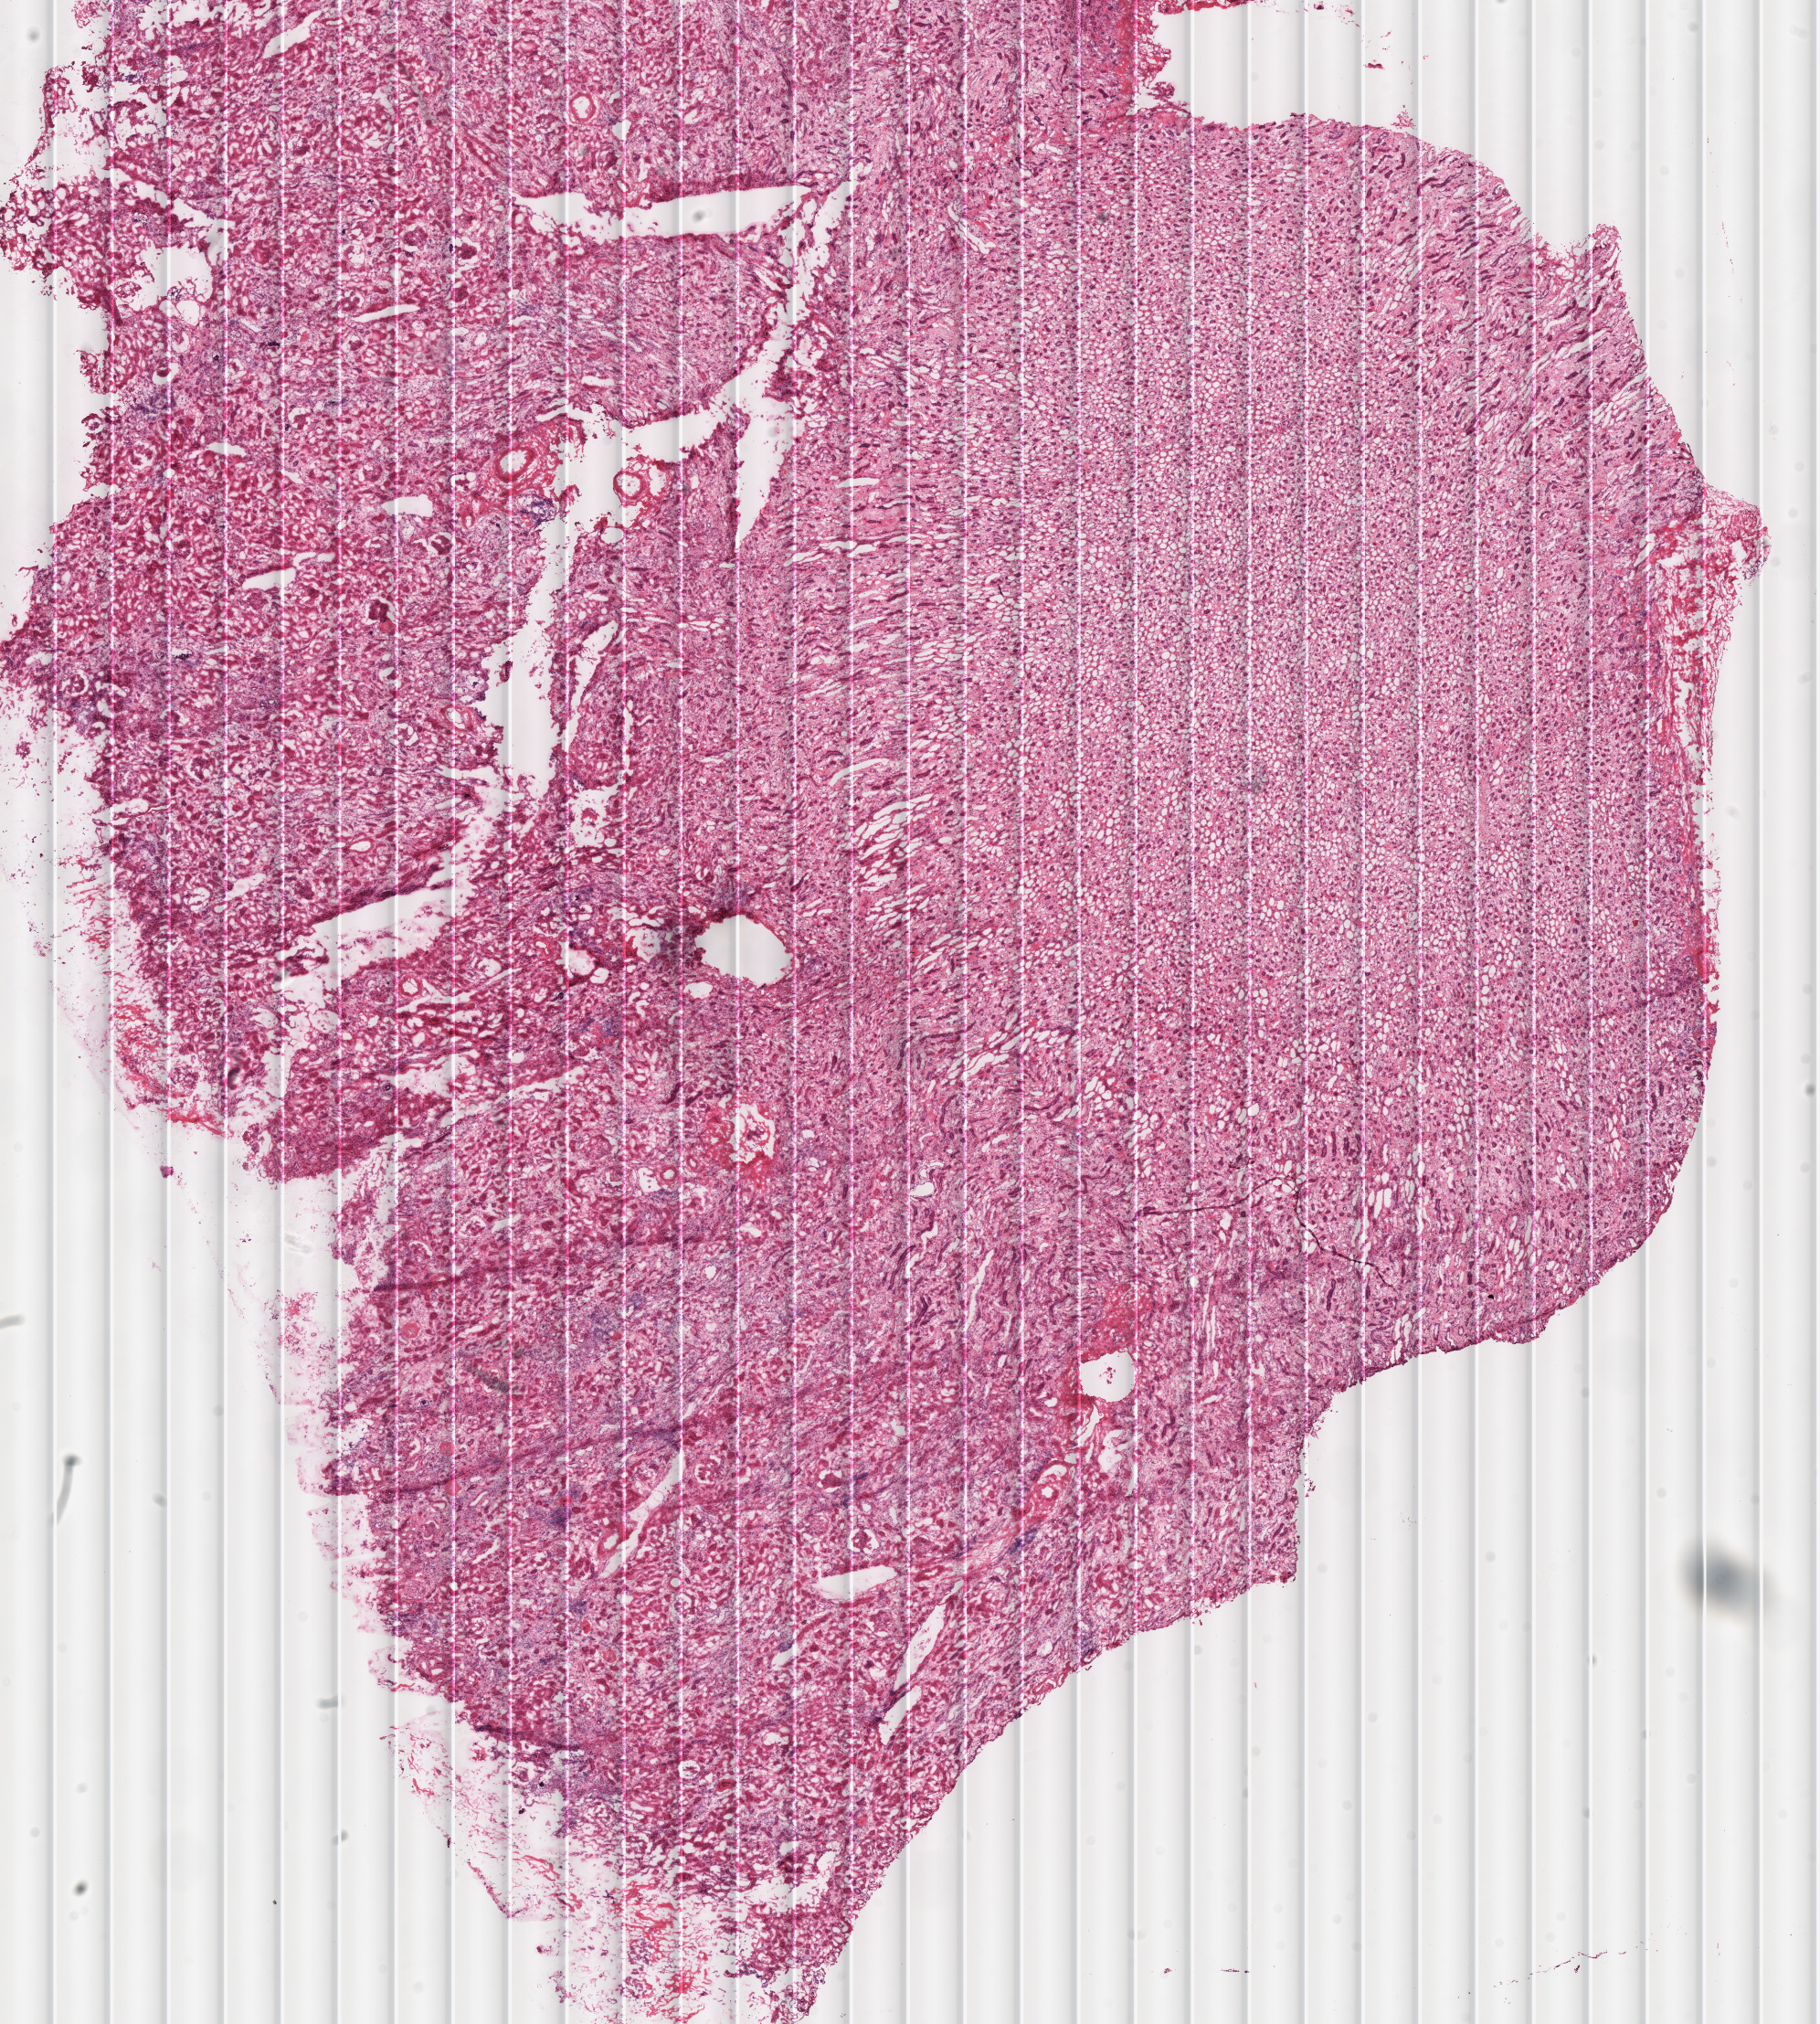
H&E-stained whole-slide image, whole scanned area (about 15.7 x 17.4 mm, from a 40x scan) shown as a low-resolution overview; frozen section from the top of the tissue portion; kidney, solid tissue normal (non-tumour tissue) sample. Patient: female, age at initial diagnosis 57 years. Infiltration values recorded for this section: lymphocyte infiltration 3%, monocyte infiltration 0%, neutrophil infiltration 0%.
This section: solid tissue normal (non-tumour) sample from the same patient. Patient diagnosis: Renal cell carcinoma, chromophobe type.